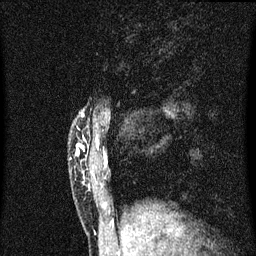
Breast MRI (dynamic contrast-enhanced), one sagittal slice; position 9 of 60 along the scan axis; dynamic contrast-enhanced series, image 2 of 3 at this slice position (ordered by acquisition); 1.5 T; TE 4.2 ms, TR 8.4 ms; 2 mm slice thickness; 256 × 256 image matrix, field of view 200 × 200 mm. Female patient, age 40 years.
Structures marked on this image (semi-automatically segmented with operator editing):
- analysis volume of interest (the breast-tissue region the enhancement analysis was run in; not a lesion): bounding box (x1, y1, x2, y2) in pixels: (78, 116, 102, 203)
- tumour enhancement mask (voxels above the 70 % enhancement threshold inside the analysis volume of interest): (78, 146, 85, 153)